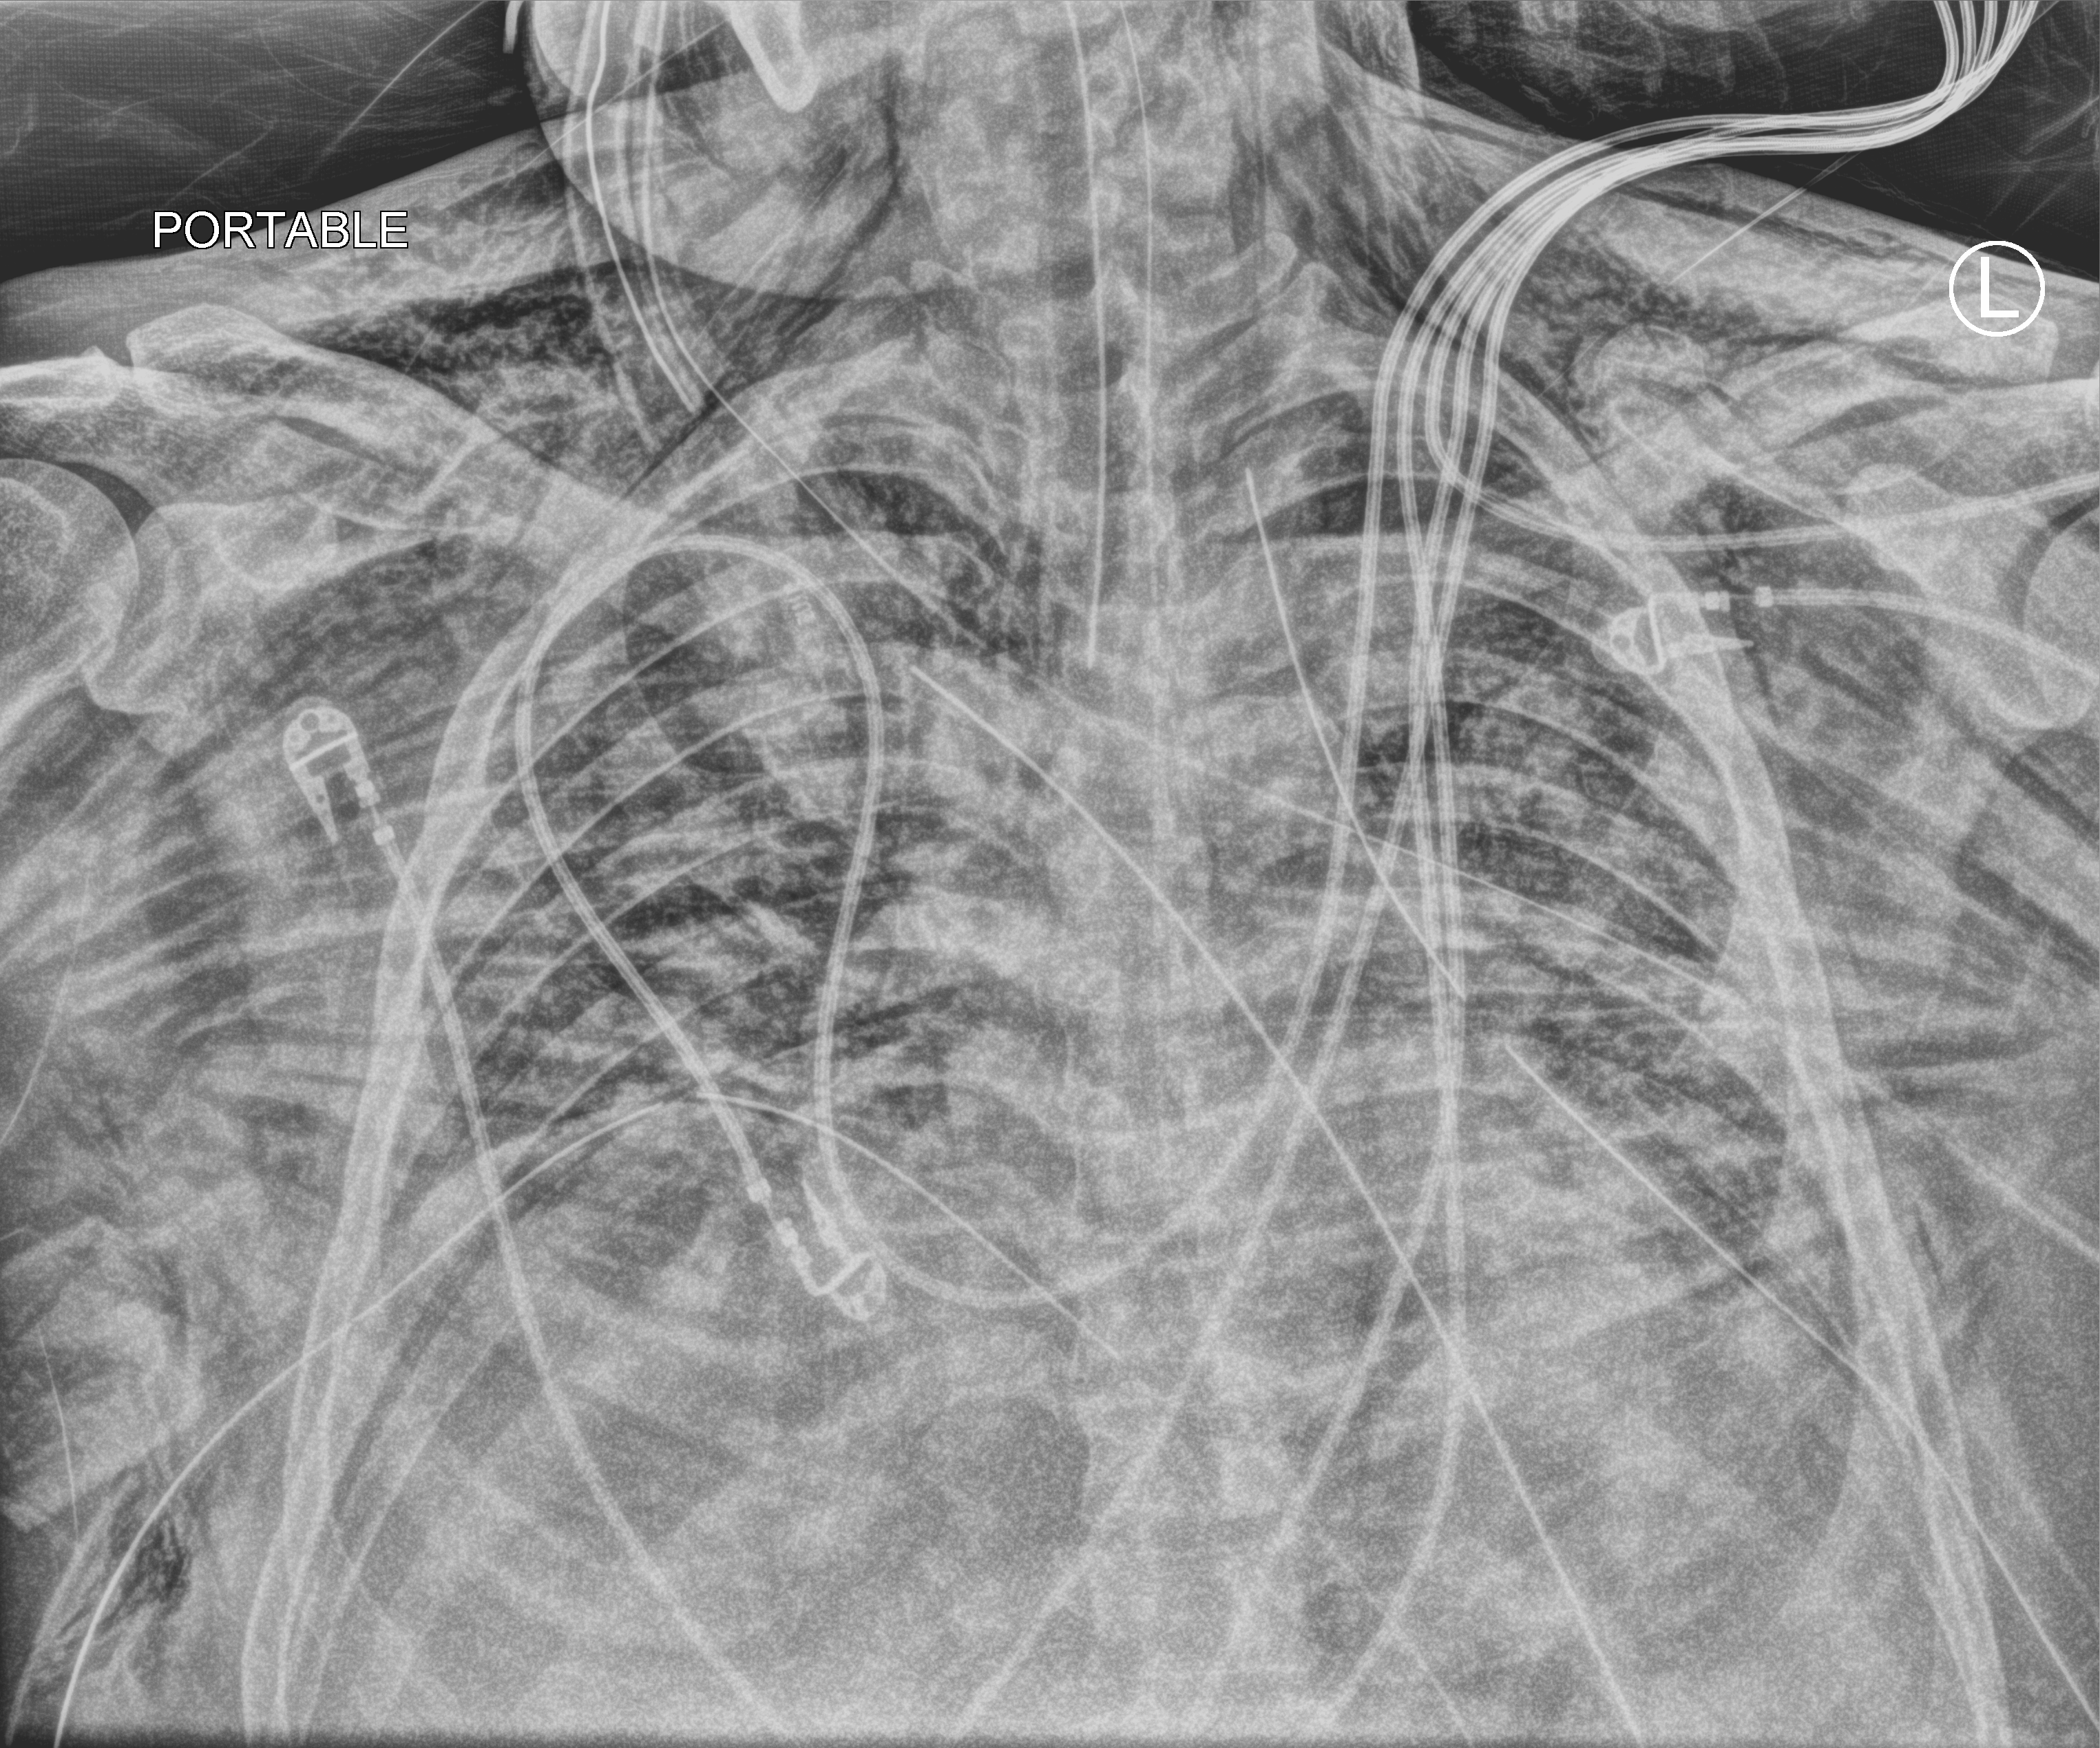
Portable chest radiograph; anteroposterior (AP) projection. Patient hospitalised with COVID-19; male, aged 18–59 years.
From the hospital-stay record, not from the radiograph (when in the stay this image was taken is not recorded): length of hospital stay: 29 days.